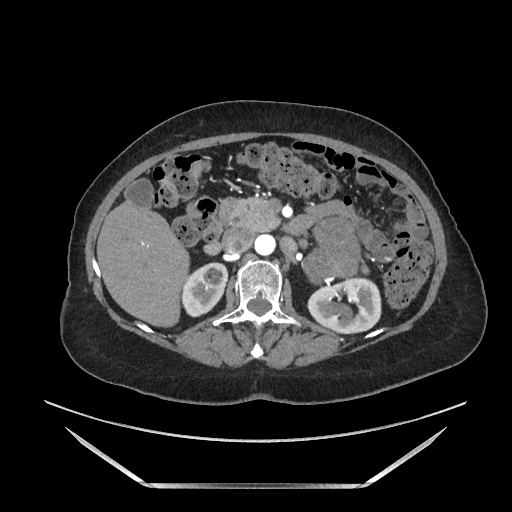
Contrast-enhanced abdominal CT, one axial slice; slice 88 of 205 in the series (ordered by position); soft-tissue window (W 400 / L 40 HU); 1.25 mm slice thickness; 512 × 512 image matrix, field of view 440 × 440 mm. Female patient. From the clinical record (not read from this slice): diagnosis: adrenocortical carcinoma; tumour side: left adrenal; tumour size at pathology: 12.5 cm.
Structures marked on this image (semi-automatic segmentation, software-assisted and operator-edited):
- mass: bounding box [x1, y1, x2, y2] px = [305, 222, 357, 280]